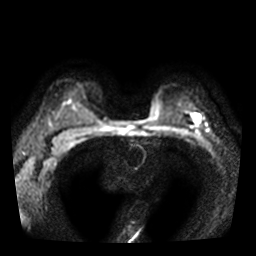
Breast MRI, one axial slice; slice 26 of 36 in the series (ordered by position); diffusion-weighted series; image 2 of 4 stored at this slice position (different b-values; order by instance number); 3 T; 5 mm slice thickness; 256 × 256 image matrix, field of view 320 × 320 mm. Female patient.
Annotated regions visible in this slice (outlined manually by an expert reader):
- tumour on diffusion-weighted imaging: bounding box [x1, y1, x2, y2] px = [194, 114, 199, 122]